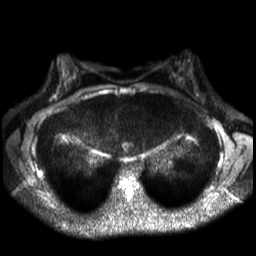
Breast MRI, one axial slice; slice 19 of 30 in the series (ordered by position); diffusion-weighted series; image 2 of 4 stored at this slice position (different b-values; order by instance number); 3 T; 4 mm slice thickness; 256 × 256 image matrix, field of view 320 × 320 mm. Female patient.
Structures marked on this image (outlined manually by an expert reader):
- tumour on diffusion-weighted imaging: box from (x=196, y=95) to (x=204, y=104) px